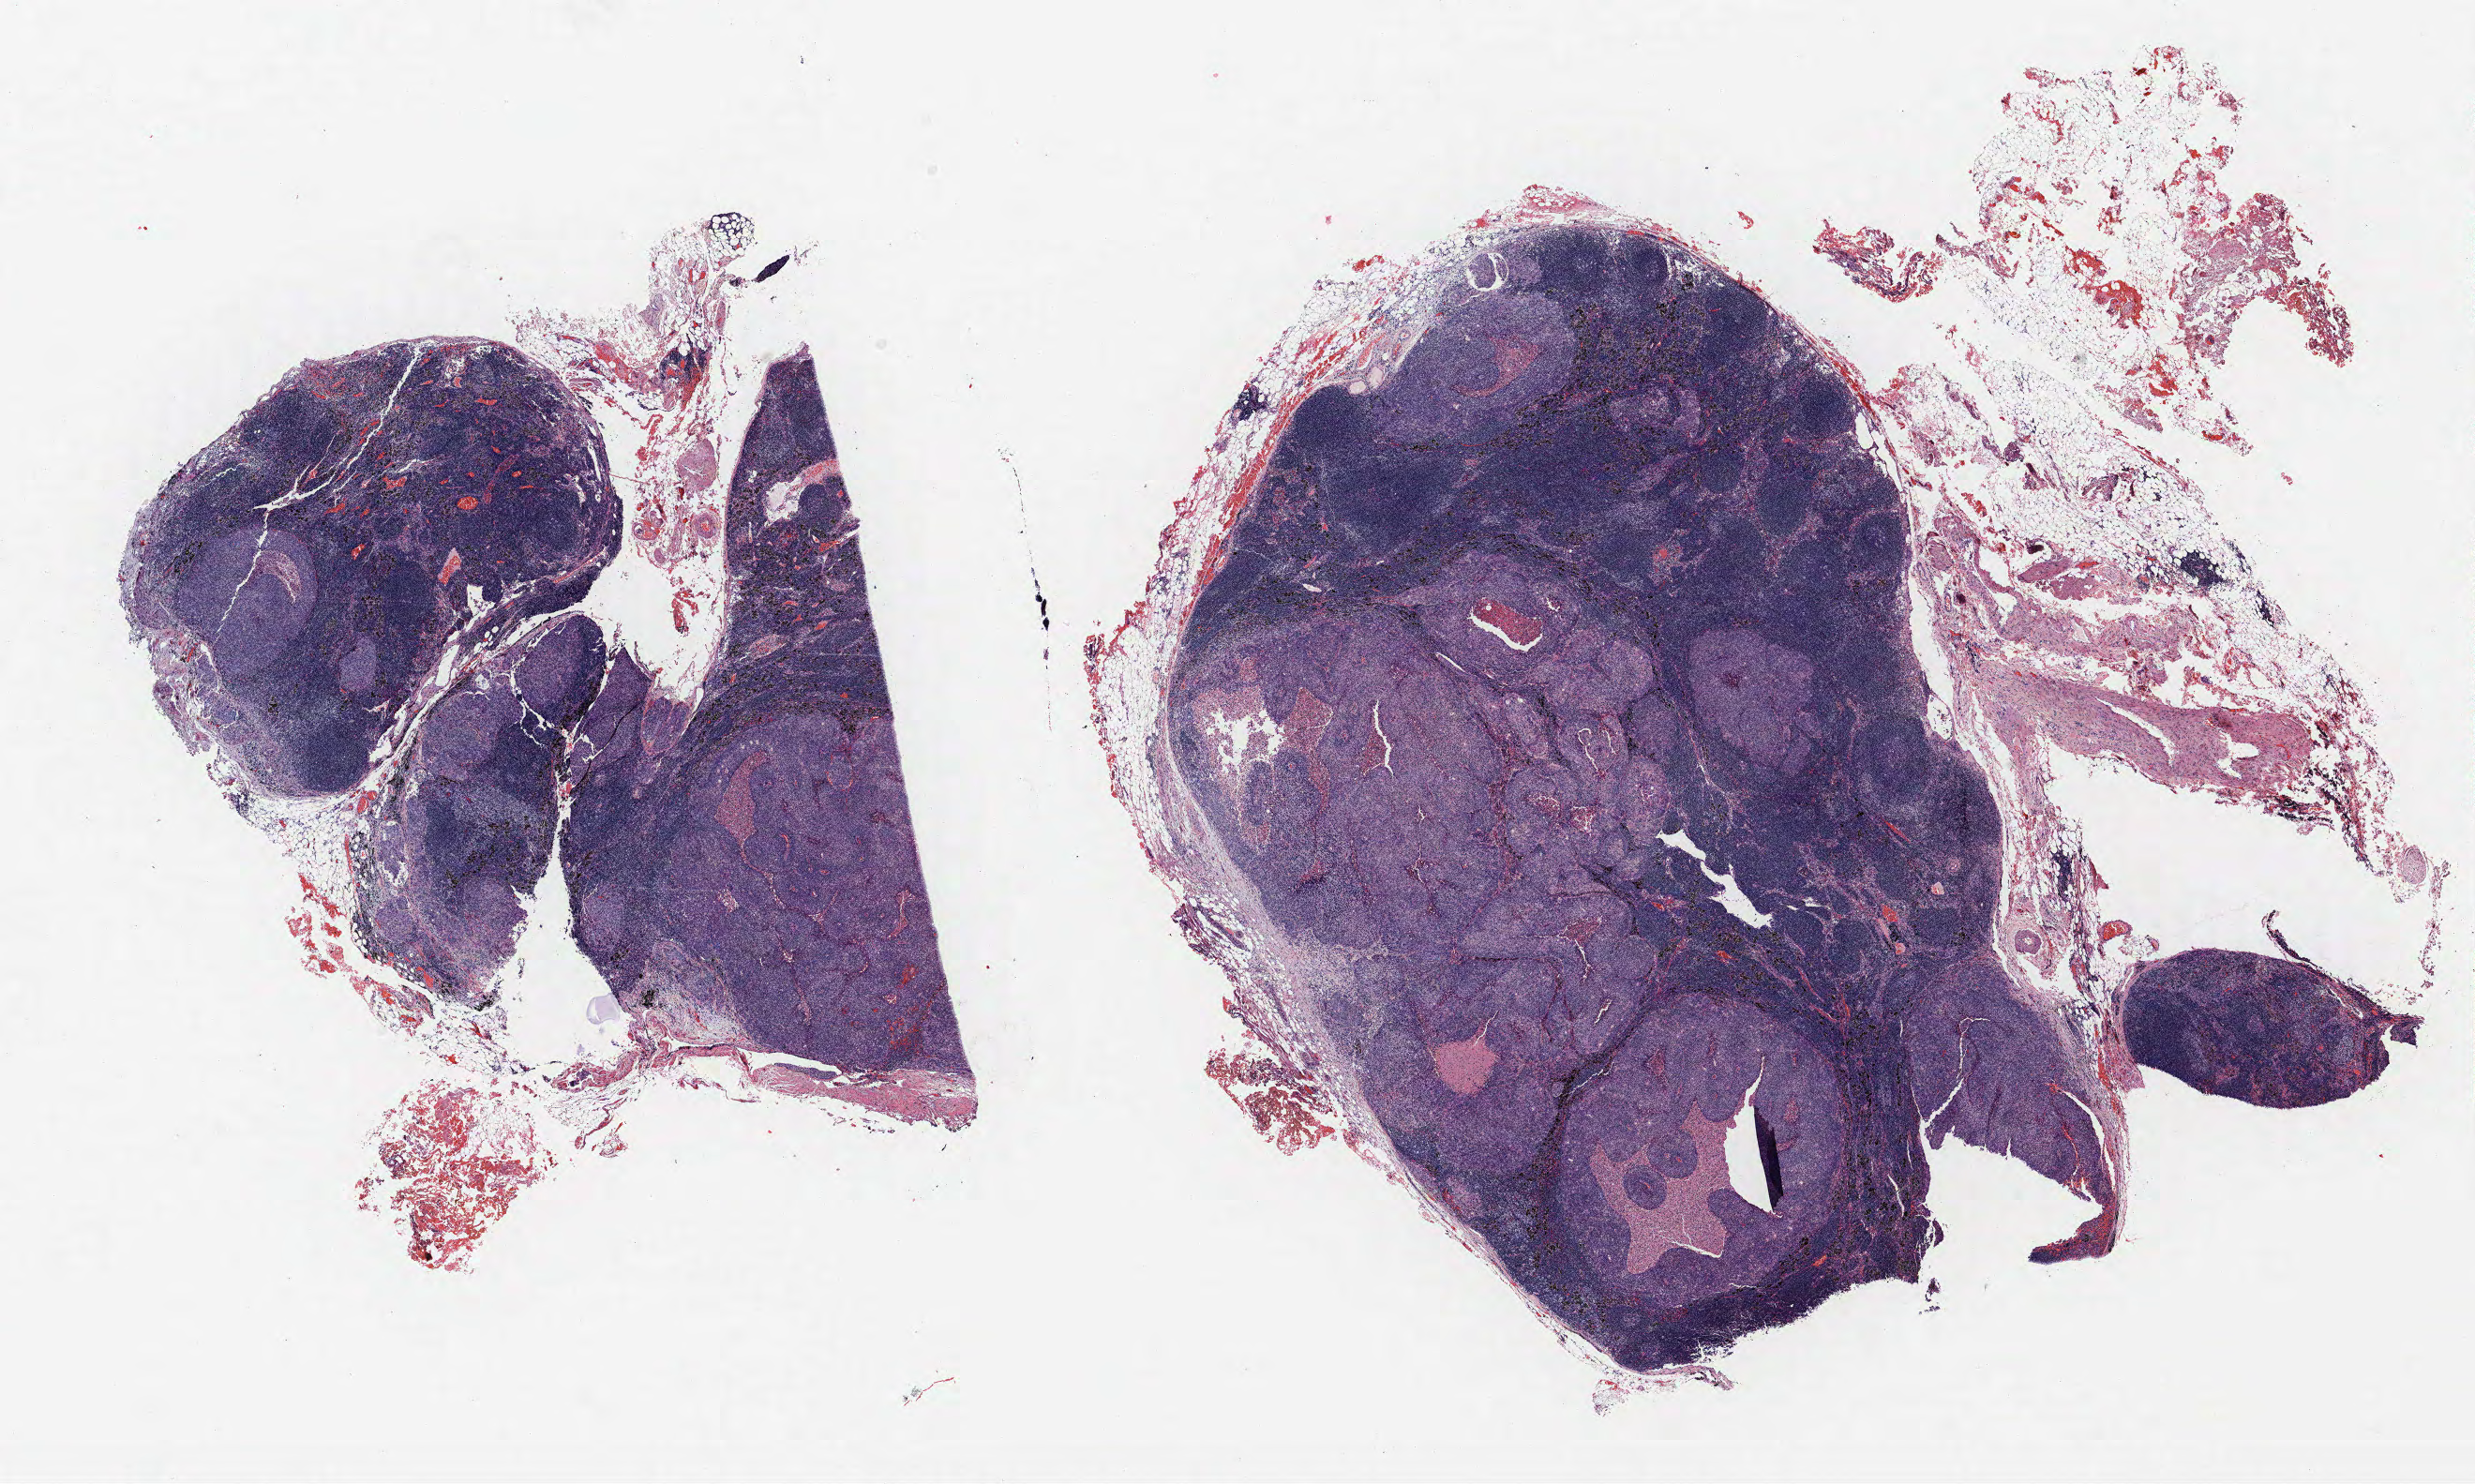
H&E-stained whole-slide image, a low-resolution overview of the entire scanned area, about 21.1 x 12.7 mm, formalin-fixed paraffin-embedded (FFPE) section, lung tissue. Male patient, aged 74 at enrolment. Former smoker at enrolment. Grade: poorly differentiated (G3).
- tumour size (pathology): 27 mm
- participant's lung-cancer diagnosis: Adenocarcinoma, NOS
- ICD-O-3 topography: upper lobe of lung (C34.1)
- stage (AJCC 6th edition): IIIA
- primary tumour location (clinical record): left upper lobe